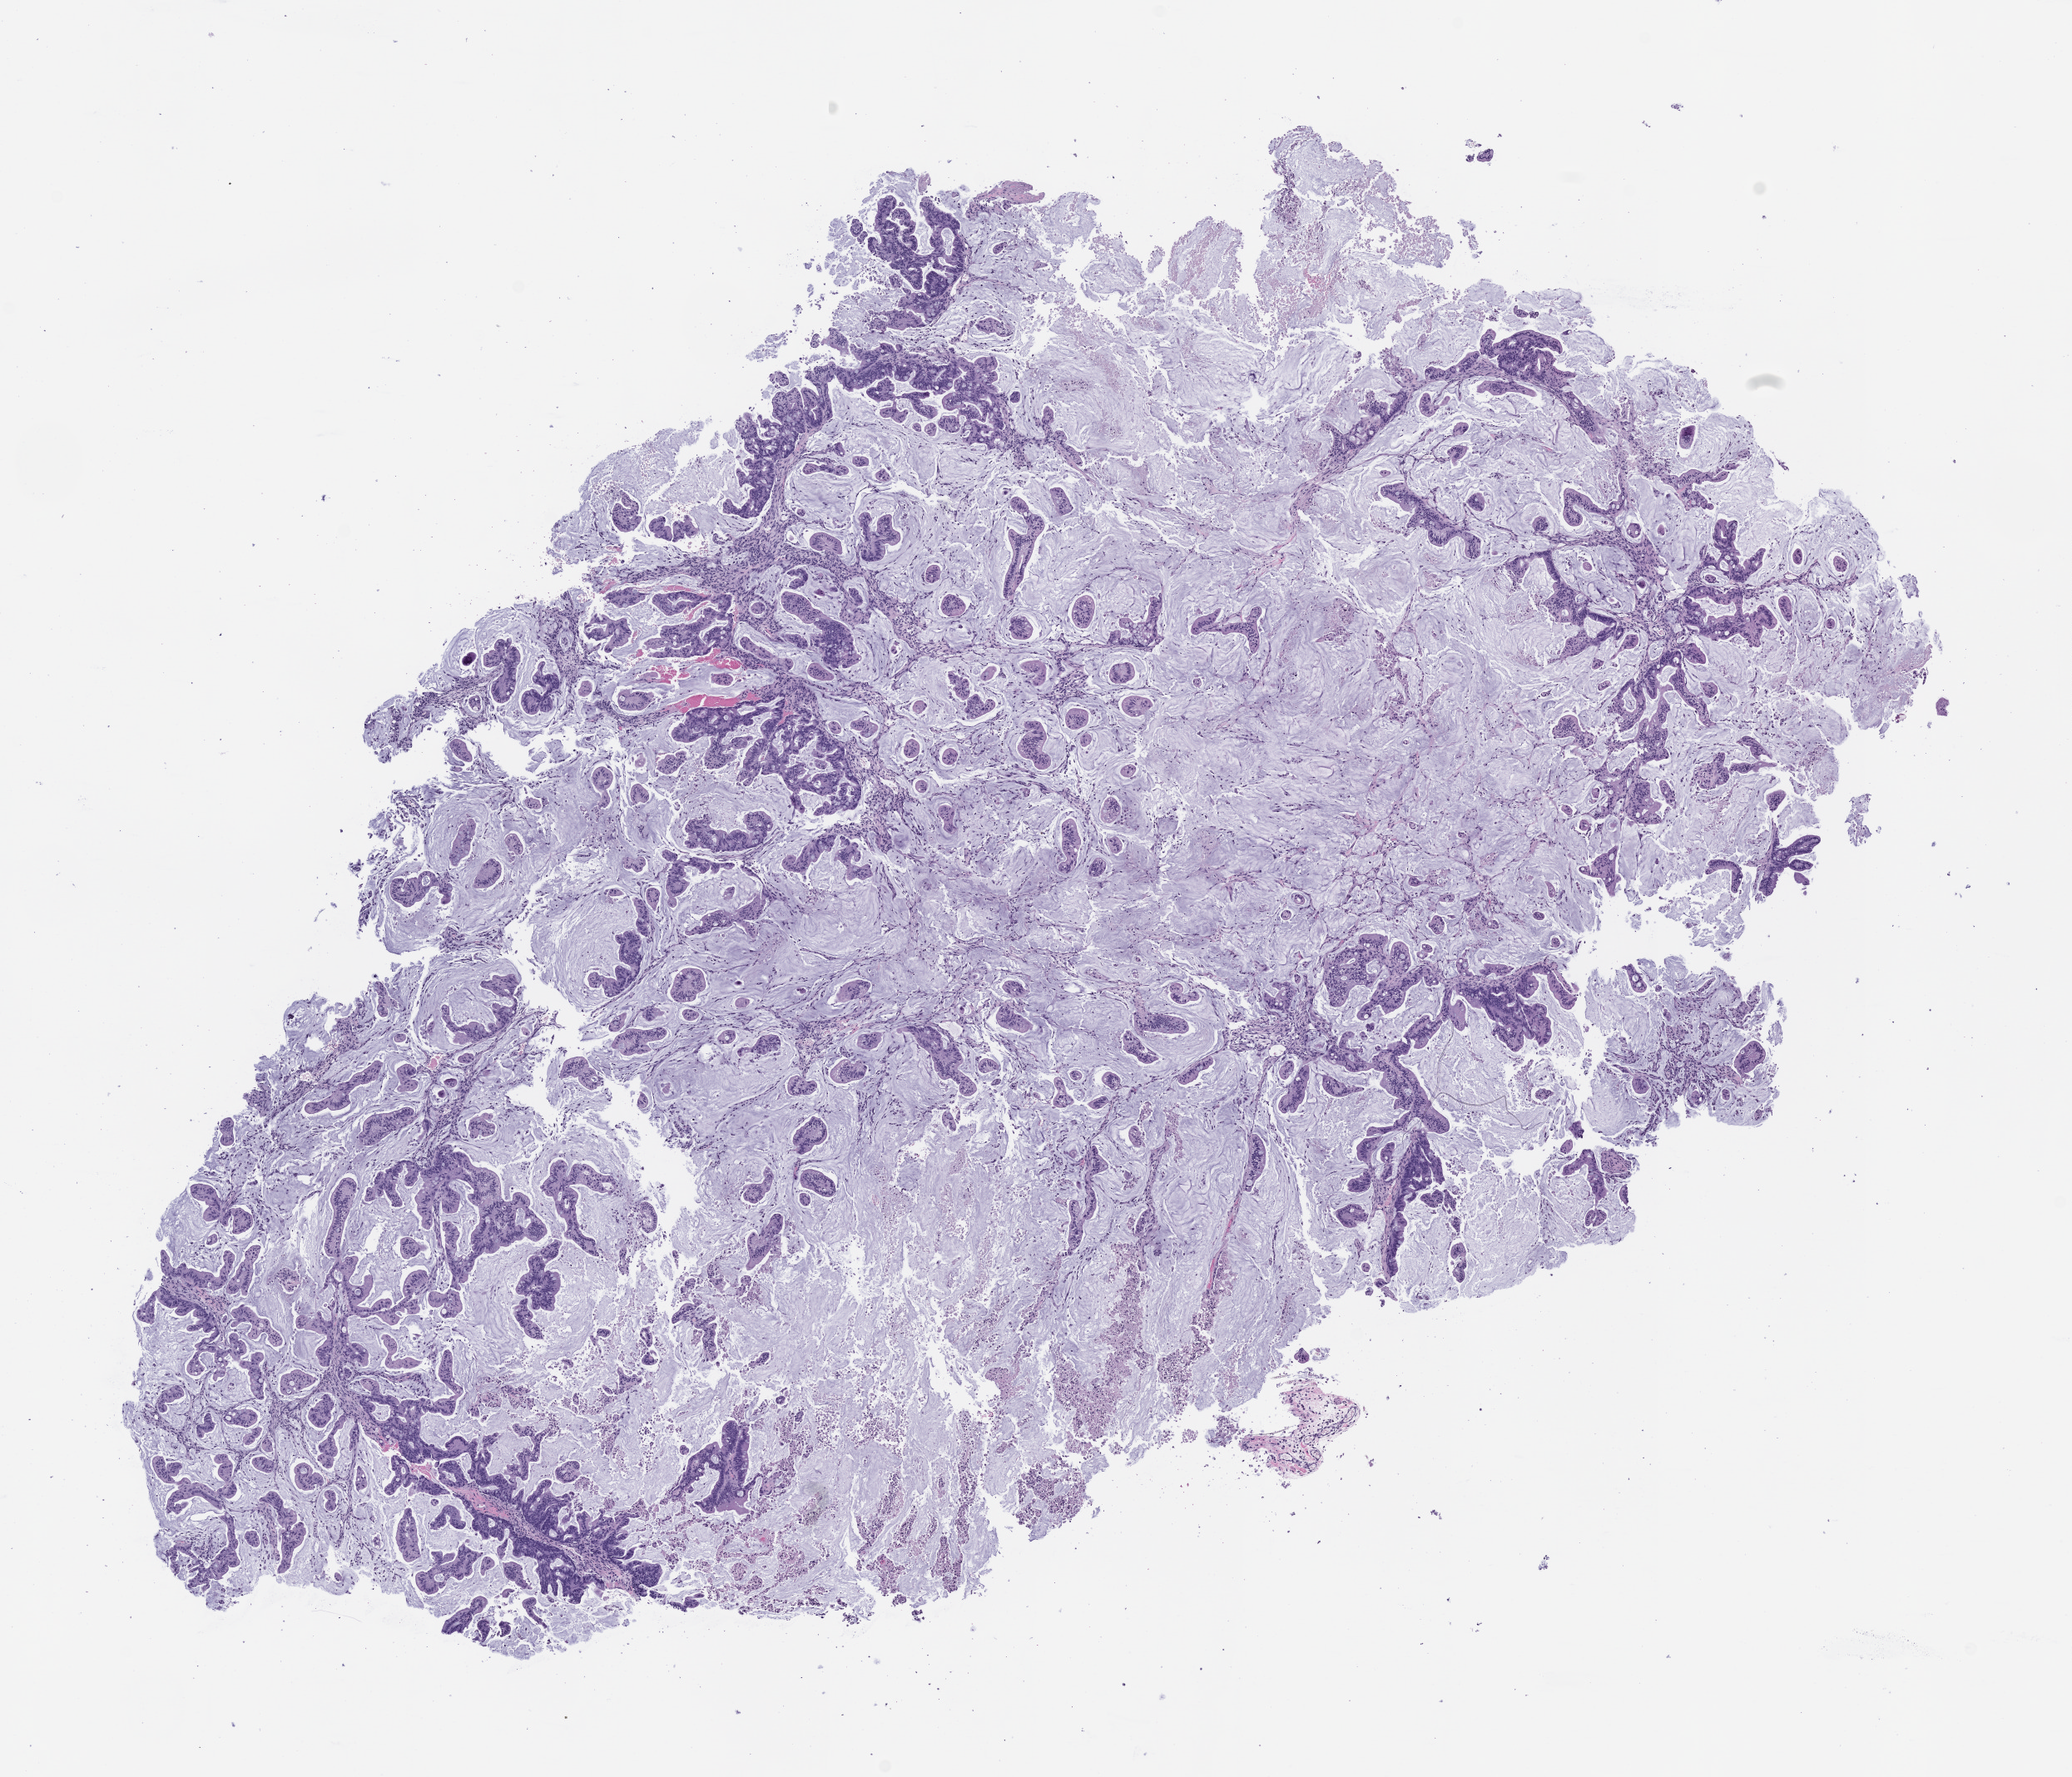
Whole-slide image, H&E: patient-derived xenograft (human tumor grown in a mouse), passage 1, a low-resolution overview of the entire scanned area, about 10.0 x 8.6 mm. Formalin-fixed paraffin-embedded section. Tumor site category: rectum.
Originating patient diagnosis: Rectal Adenocarcinoma.